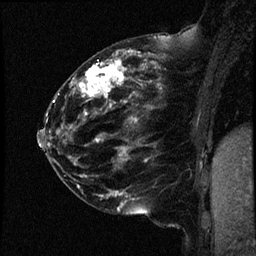
Breast MRI (dynamic contrast-enhanced), one sagittal slice. Position 22 of 44 along the scan axis. Dynamic contrast-enhanced study with each time point stored as its own series, time point 2 of 4 at this slice position (early post-contrast, ordered by acquisition time). 1.5 T. TE 4.2 ms, TR 17.7 ms. 256 × 256 image matrix. Patient: female, 52 years. From the clinical record (not read from this slice): setting: breast cancer imaged before/during neoadjuvant chemotherapy; receptor status: HR-positive, HER2-negative.
Structures marked on this image (semi-automatically segmented with operator editing):
- analysis volume of interest (the breast-tissue region the enhancement analysis was run in; not a lesion): bounding box [x1, y1, x2, y2] px = [47, 48, 163, 147]
- tumour enhancement mask (voxels above the 100 % enhancement threshold inside the analysis volume of interest): [71, 51, 148, 141]